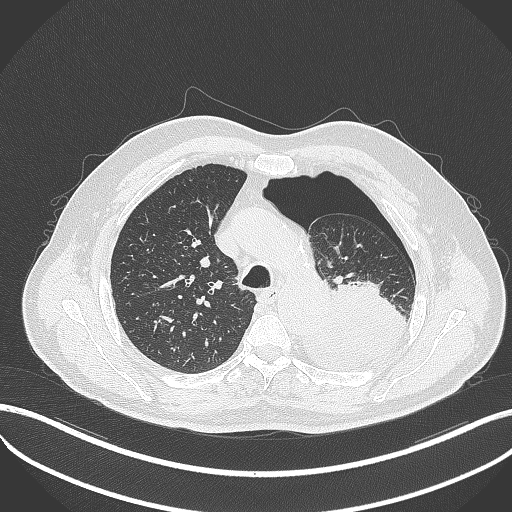
Chest CT, one axial slice. Position 372 of 464 along the scan axis. Reconstruction kernel B70f. Lung window (W 1500 / L -600 HU). 1 mm slice thickness. 512 × 512 image matrix, field of view 400 × 400 mm. Patient: male, 76 years. Case-level facts recorded for this patient, not image findings: clinical TNM (as recorded): T3 N0 M1b.
Structures marked on this image (rectangle marked by the reading radiologist):
- lung tumour (recorded histology: adenocarcinoma): bounding box (x1, y1, x2, y2) in pixels: (292, 280, 408, 374)